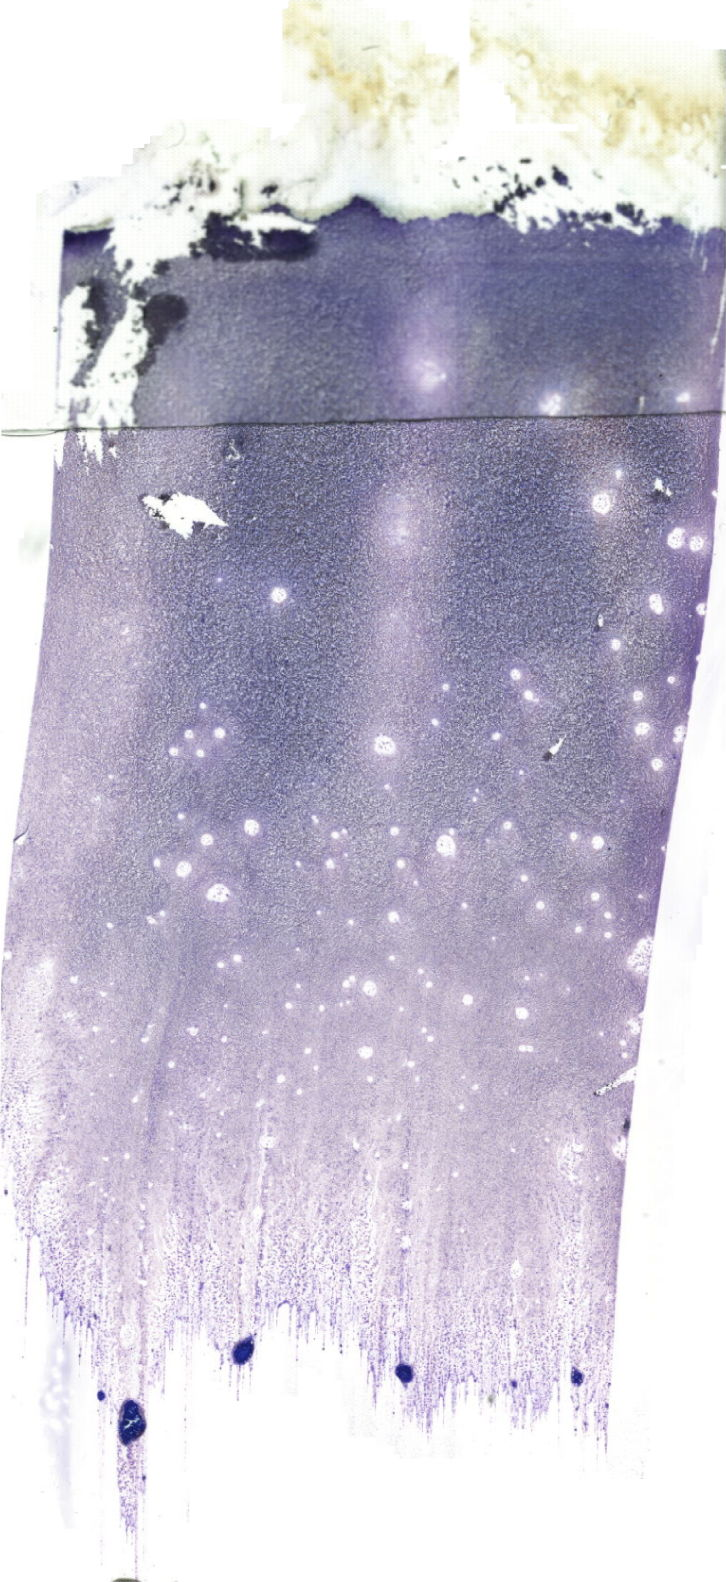
Bone marrow aspirate smear, May-Grünwald–Giemsa stain, whole-slide image, low-resolution overview of the scanned area, about 20.6 x 44.8 mm. Patient sex: female.
* diagnosis: Acute Myeloid Leukemia with Maturation